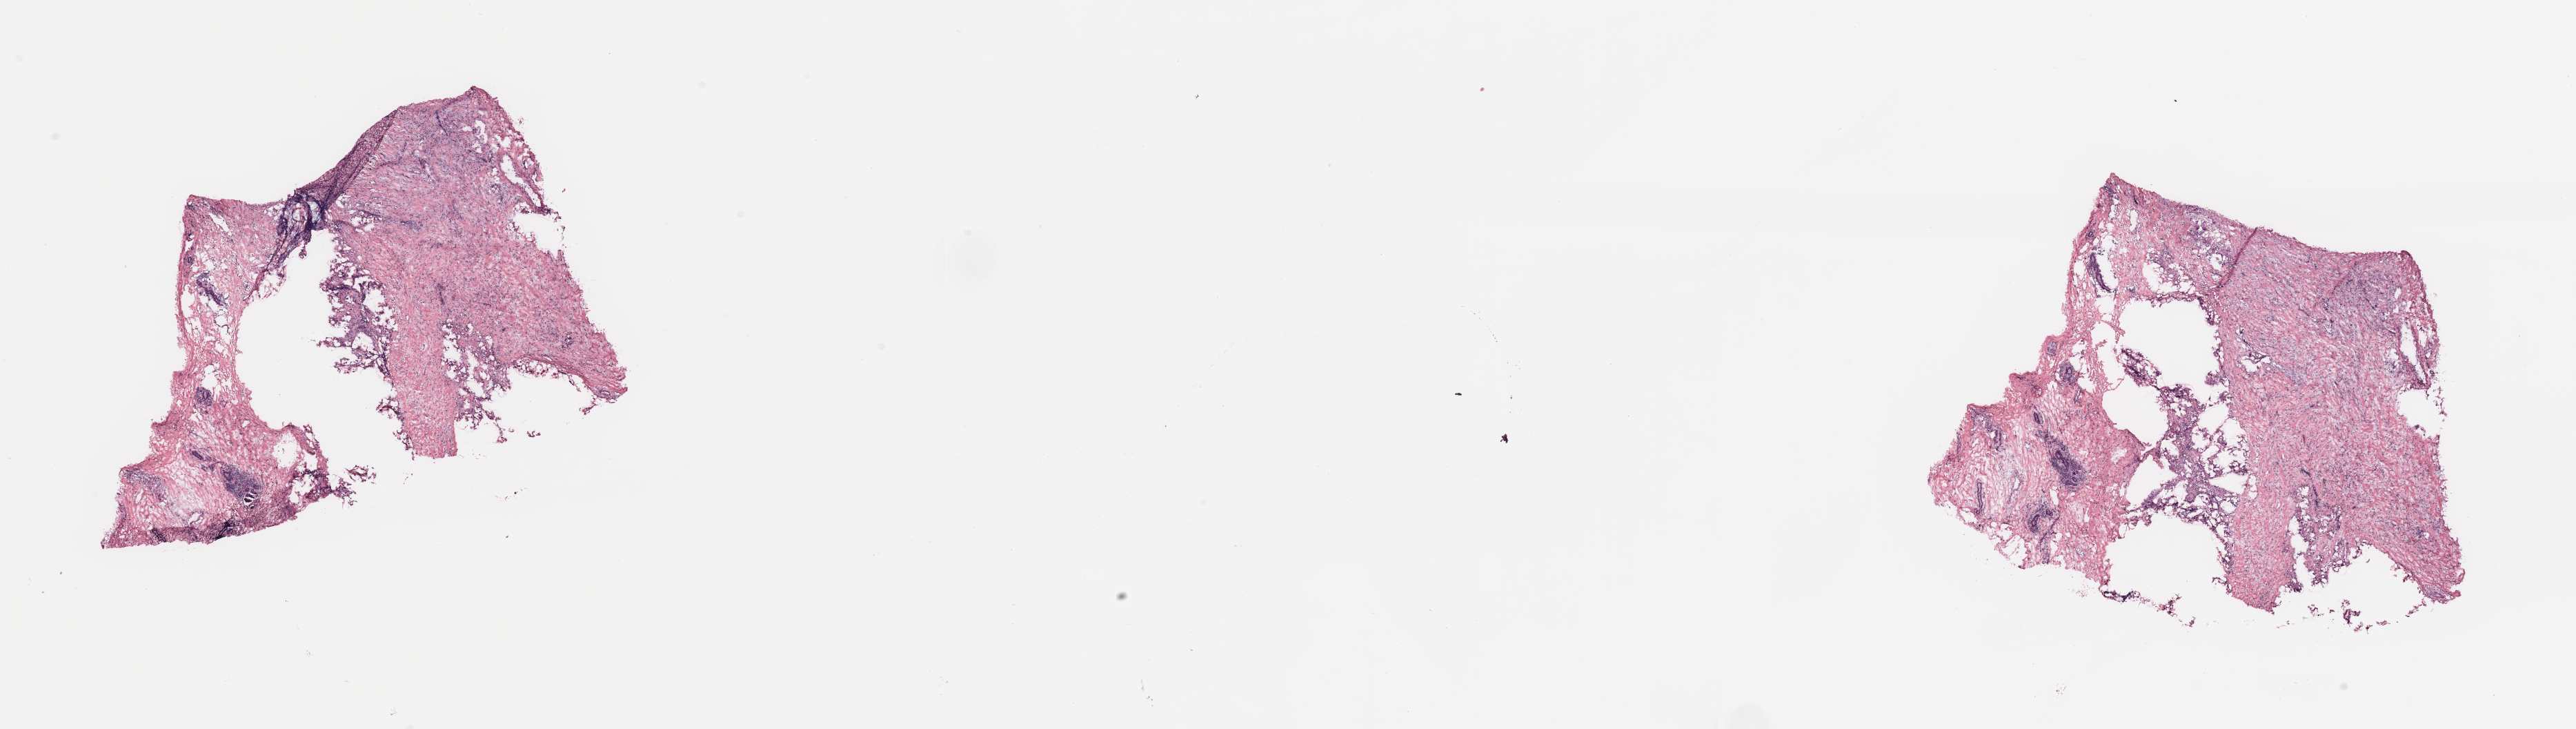
Hematoxylin and eosin (H&E) stained whole-slide image — a low-resolution overview of the entire scanned area, about 29.5 x 8.4 mm (from a 20x scan); breast, tissue type not recorded.
Patient diagnosis (cohort enrolment): breast cancer (breast).